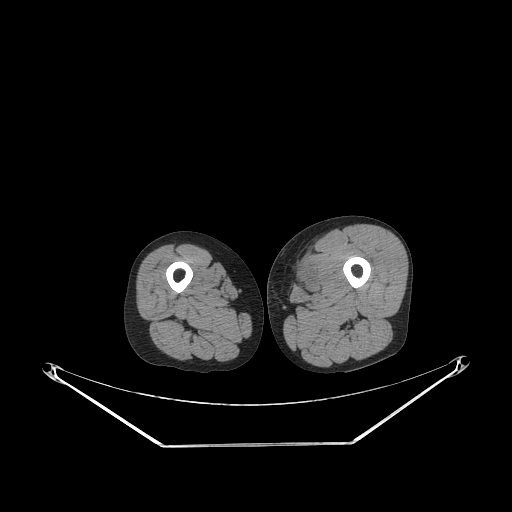
CT of an extremity soft-tissue mass (from a PET/CT study), one axial slice. Slice 230 of 267 in the series (ordered by position). 140 kVp. Soft-tissue window (W 400 / L 40 HU). 512 × 512 image matrix. Male patient. Case-level facts recorded for this patient, not image findings: histological type: pleiomorphic leiomyosarcoma; grade: high; site of the primary tumour: left thigh.
Structures marked on this image (expert contour drawn on MRI and transferred to this co-registered scan by the dataset authors):
- gross tumour volume including surrounding oedema: bounding box <290,256,314,291> (left, top, right, bottom; pixels)
- gross tumour volume (mass): <295,272,311,289>